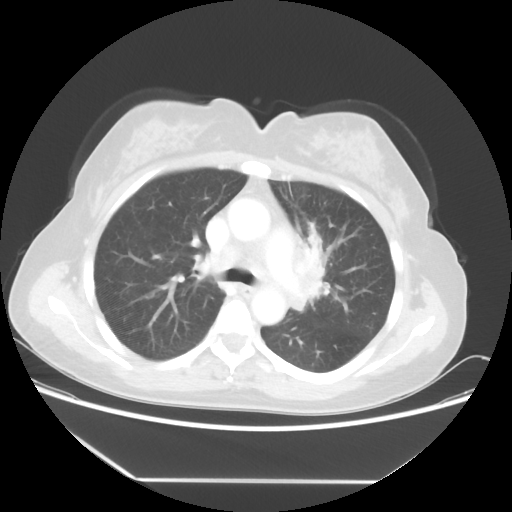
Chest CT, one axial slice; reconstruction kernel STANDARD; lung window (W 1500 / L -600 HU); 5 mm slice thickness; 512 × 512 image matrix, field of view 390 × 390 mm. Female patient, age 50 years. Case-level facts recorded for this patient, not image findings: clinical TNM (as recorded): T2 N3 M0.
Structures marked on this image (rectangle marked by the reading radiologist):
- lung tumour (recorded histology: adenocarcinoma): box from (x=280, y=219) to (x=345, y=329) px